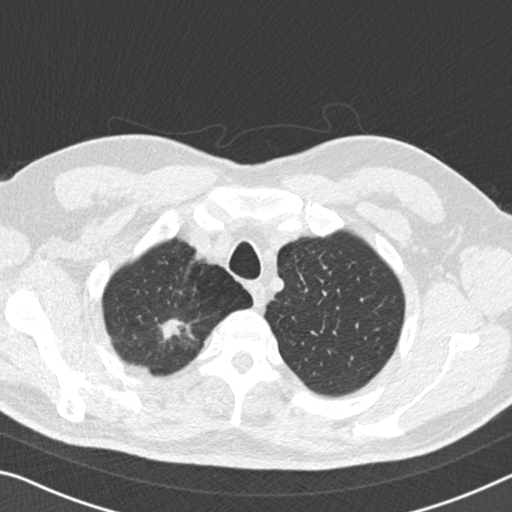
Low-dose screening chest CT, one axial slice; slice 144 of 167 in the series (ordered by position); reconstruction kernel B30f; 120 kVp; lung window (W 1500 / L -600 HU); 512 × 512 image matrix, field of view 336 × 336 mm.
Annotated regions visible in this slice (manually delineated by an expert):
- lesion 1 (tumor, upper lobe of right lung): bounding box (x1, y1, x2, y2) in pixels: (162, 319, 183, 339)